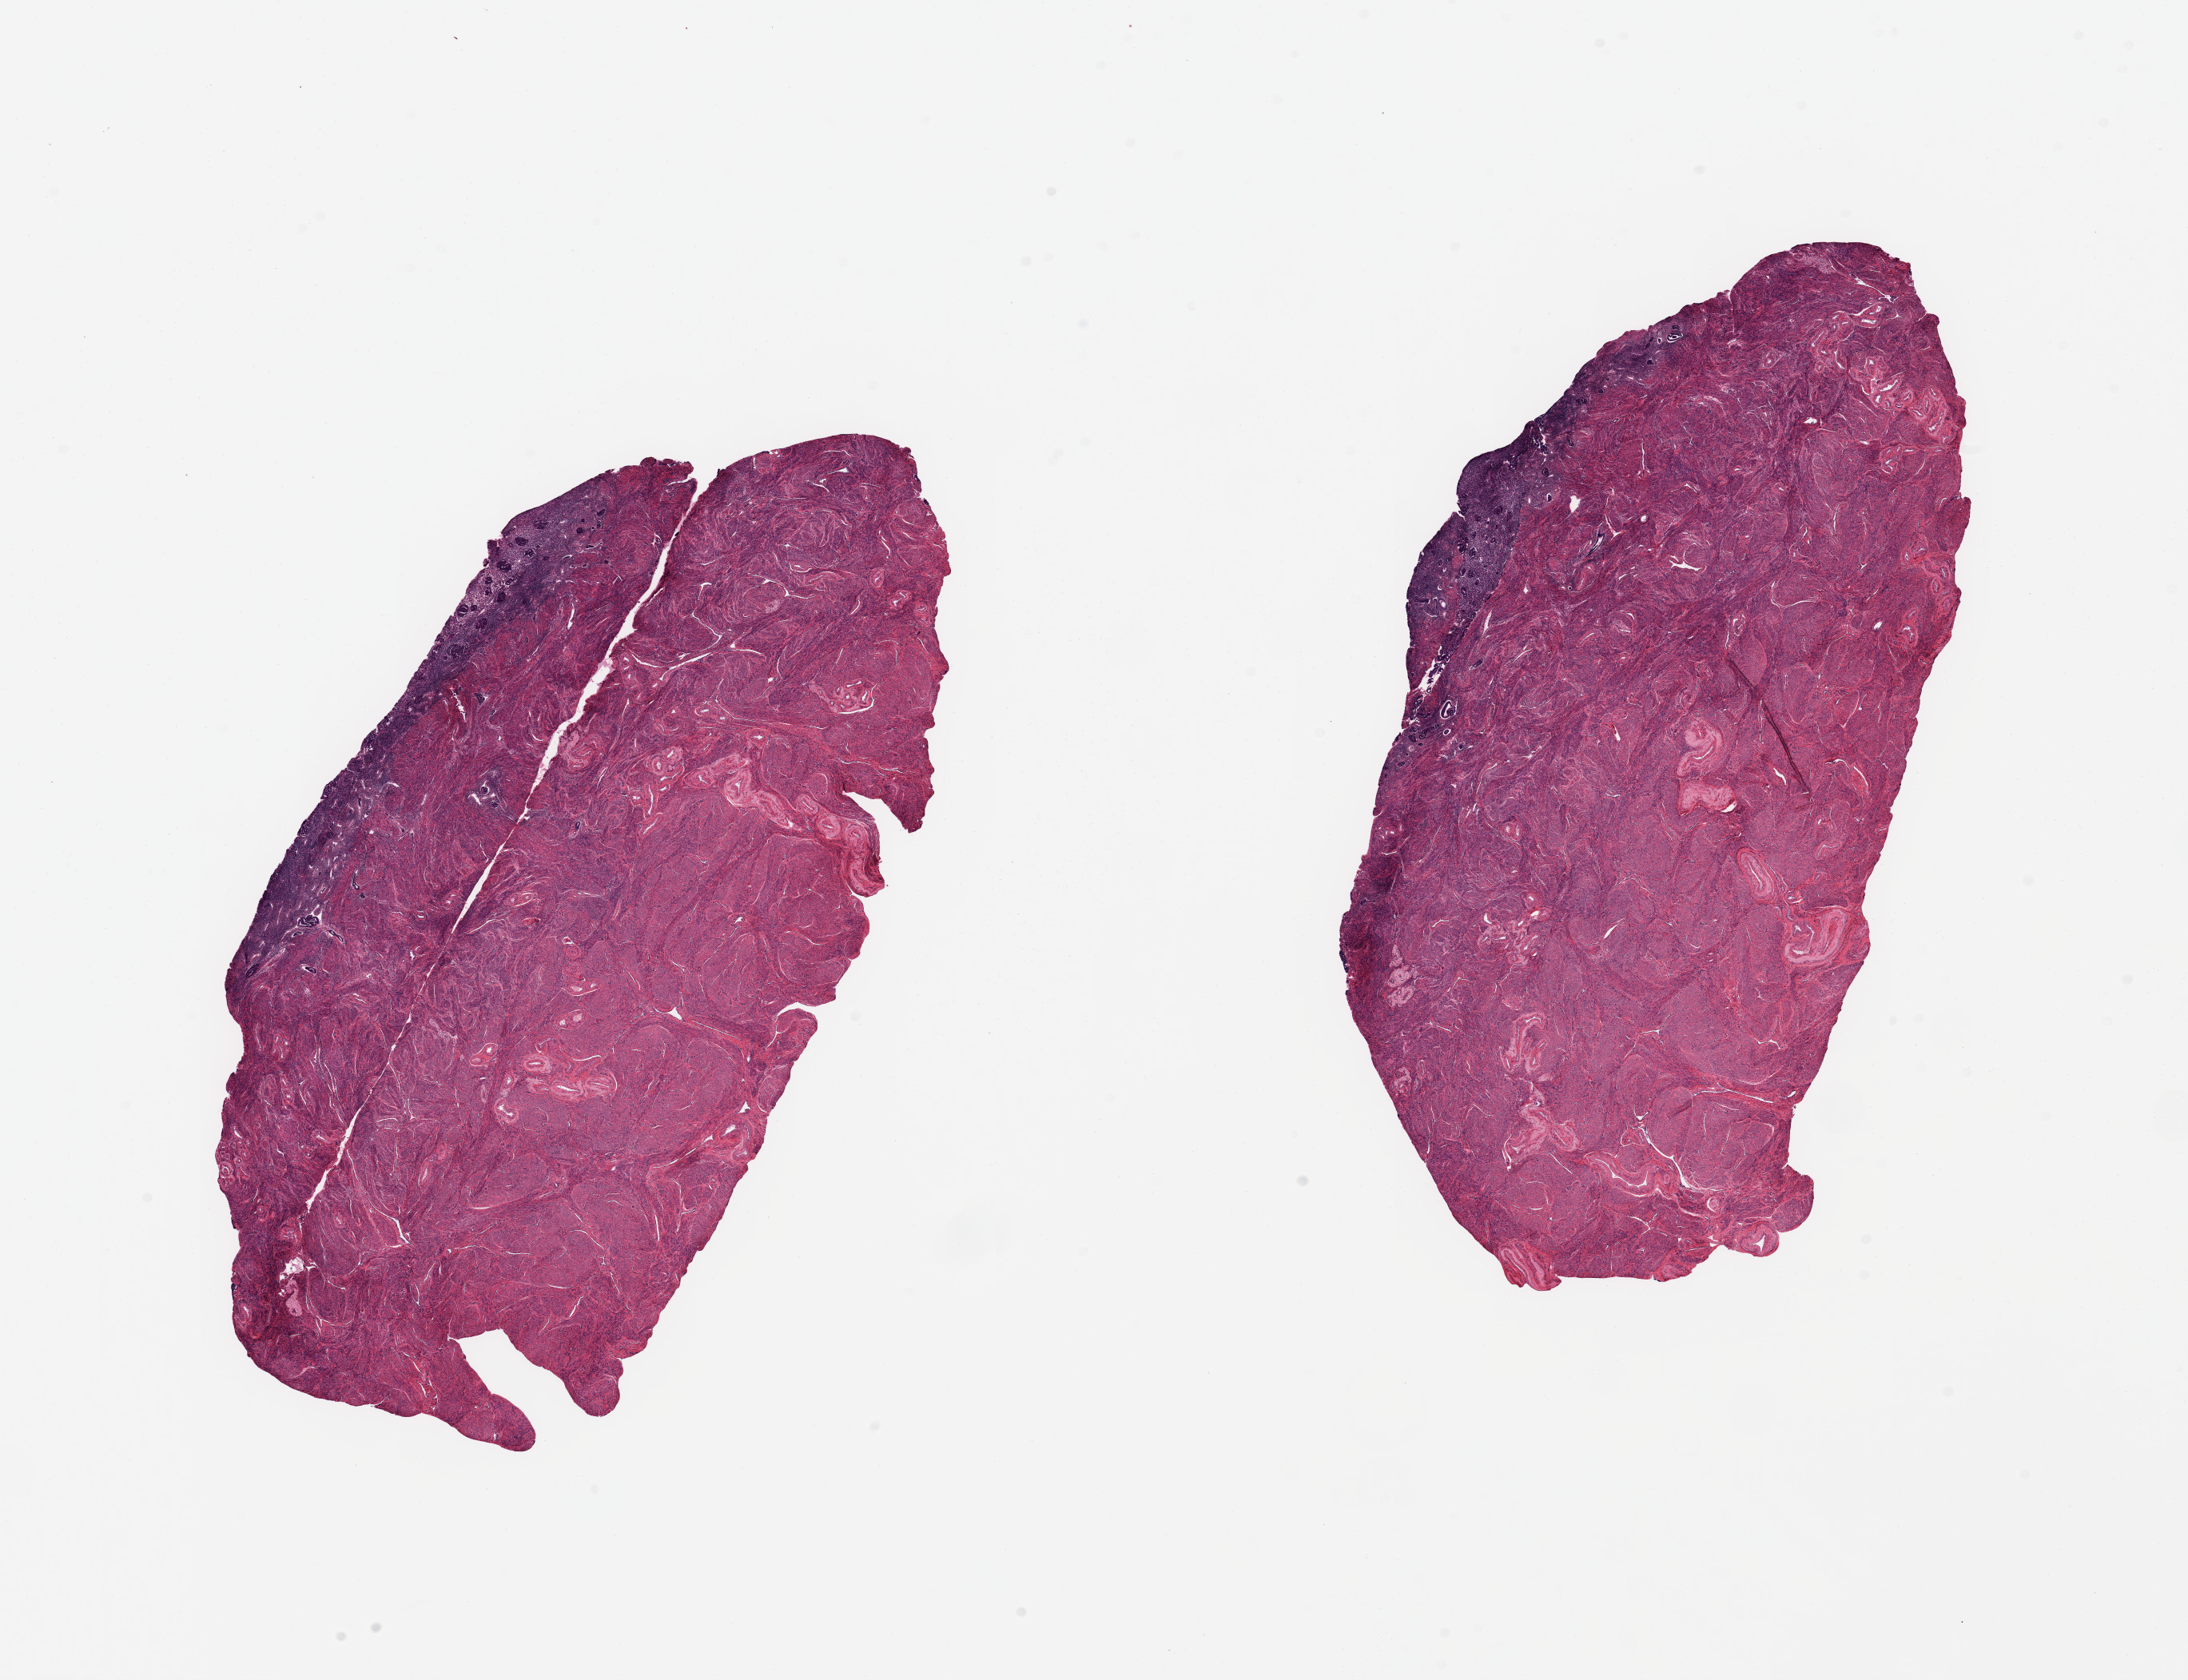
Hematoxylin and eosin (H&E) whole-slide image, whole scanned area (about 21.7 x 16.6 mm) shown as a low-resolution overview, PAXgene-fixed paraffin-embedded (PFPE) section, sampled site (target tissue): uterus, donor tissue sample. Female donor.
Review note (as recorded): 2 pieces, mainly myometrium; focal inactive/basalis endometrium, foci up to ~0.6mm.